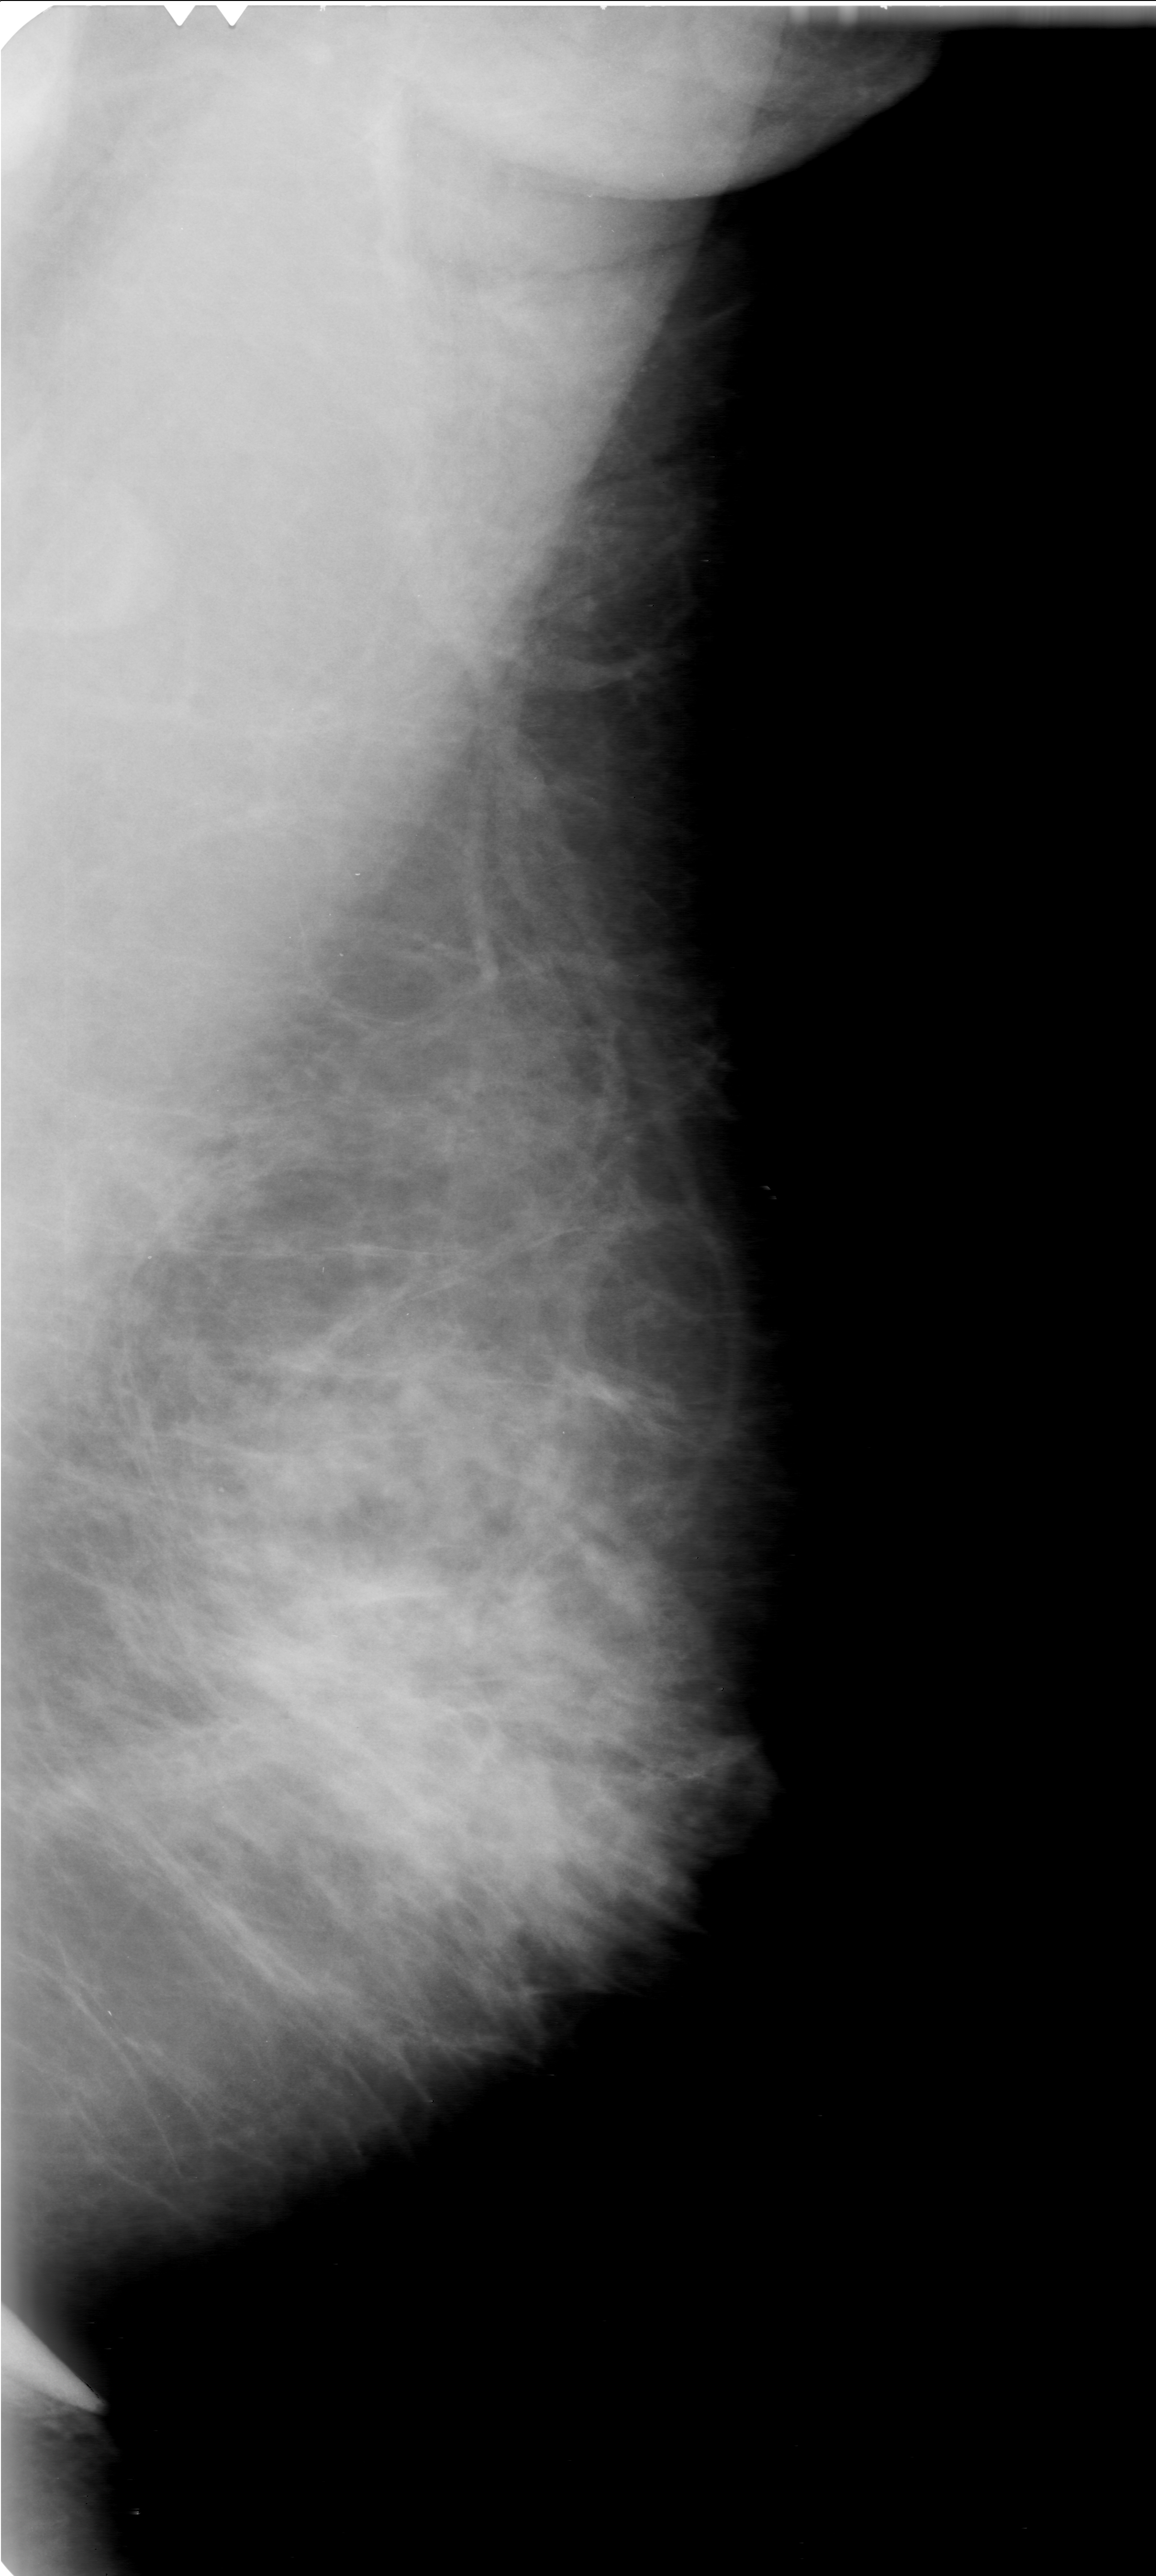
Mammogram (digitized film); left breast; mediolateral oblique (MLO) view; BI-RADS breast density category 3 (scale 1–4); 1156 × 2576 image matrix.
Marked abnormalities (boxes around the expert regions of interest):
- mass, shape architectural distortion; BI-RADS assessment category 0 (incomplete: needs additional imaging); subtlety rating 5 on a 1 (subtle) to 5 (obvious) scale; pathology (as recorded): malignant: bounding box [x1, y1, x2, y2] px = [226, 1550, 499, 1823]